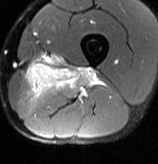
MRI of an extremity soft-tissue mass, one axial slice; position 25 of 70 along the scan axis; T2-weighted fat-saturated; MR volume resampled by the dataset authors to the PET/CT grid (not the native acquisition matrix); 3.27 mm slice thickness; 158 × 164 image matrix, field of view 154 × 160 mm. Male patient. From the clinical record (not read from this slice): histological type: extraskeletal osteosarcoma; grade: high; site of the primary tumour: left adductur.
Outlined on this slice (expert contour drawn on MRI and transferred to this co-registered scan by the dataset authors):
- gross tumour volume (mass): bounding box [x1, y1, x2, y2] px = [24, 64, 101, 97]